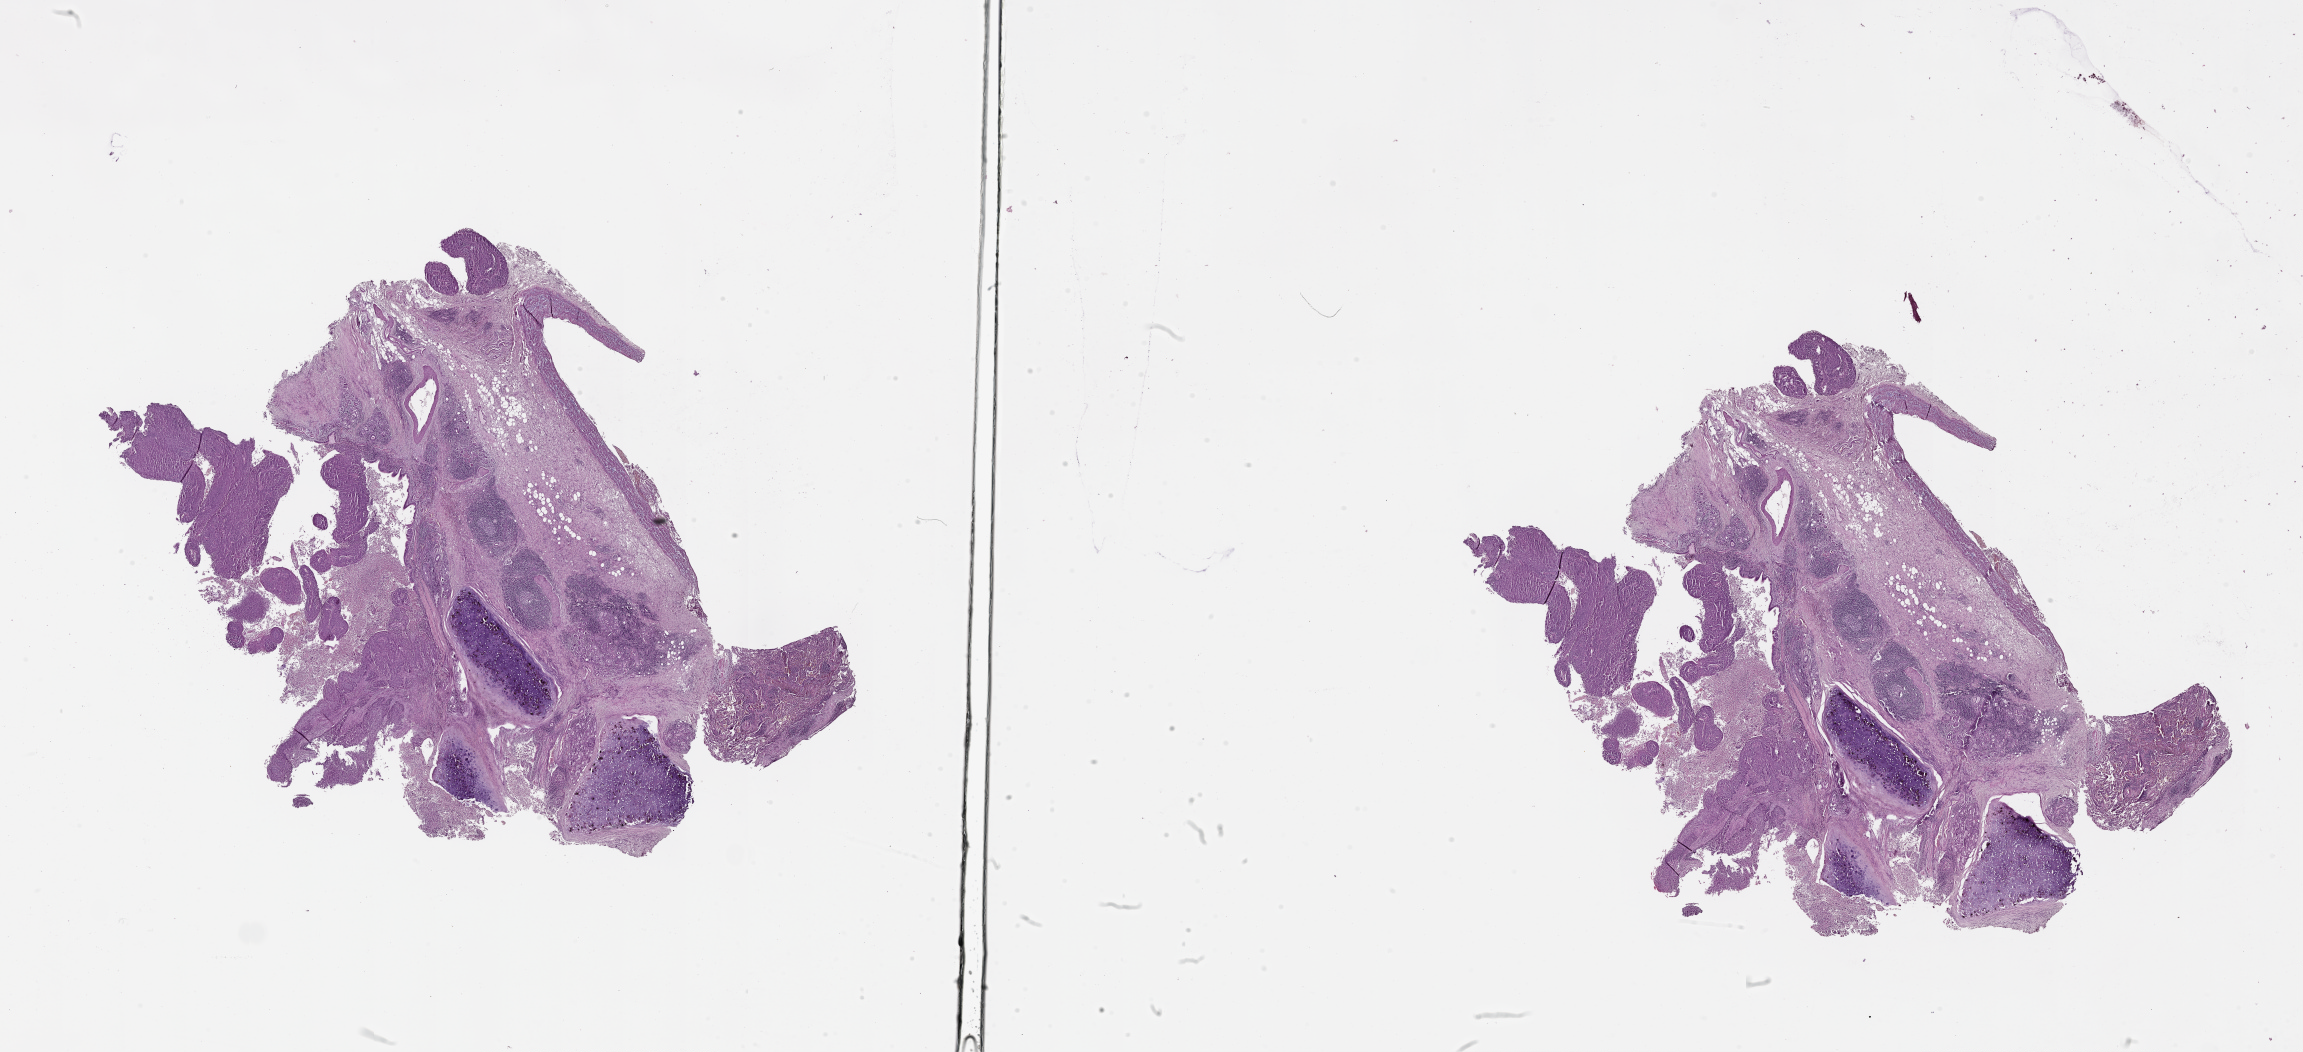
Hematoxylin and eosin (H&E) stained whole-slide image, a low-resolution overview of the entire scanned area, about 37.1 x 16.9 mm. Lung, tumour tissue. 63-year-old female patient.
Patient diagnosis (cohort enrolment): squamous cell carcinoma (lung).